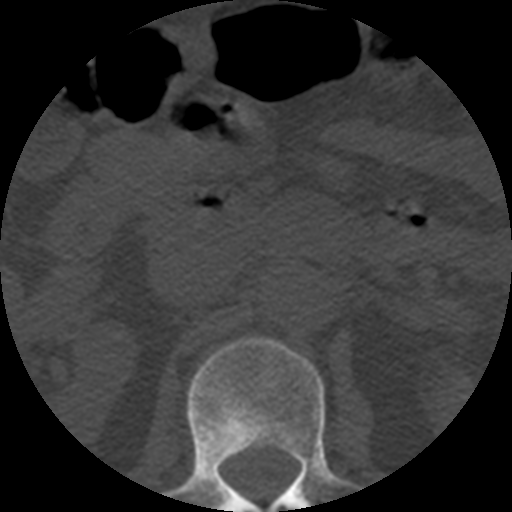
CT including the spine, one axial slice. Position 183 of 508 along the scan axis. Reconstruction kernel STANDARD. 120 kVp. Bone window (W 1800 / L 400 HU). 512 × 512 image matrix. Patient age 57 years. Case-level facts recorded for this patient, not image findings: primary cancer: prostate.
Annotated regions visible in this slice (semi-automatic segmentation, software-assisted and operator-edited):
- L1 vertebra: box from (x=165, y=338) to (x=359, y=512) px